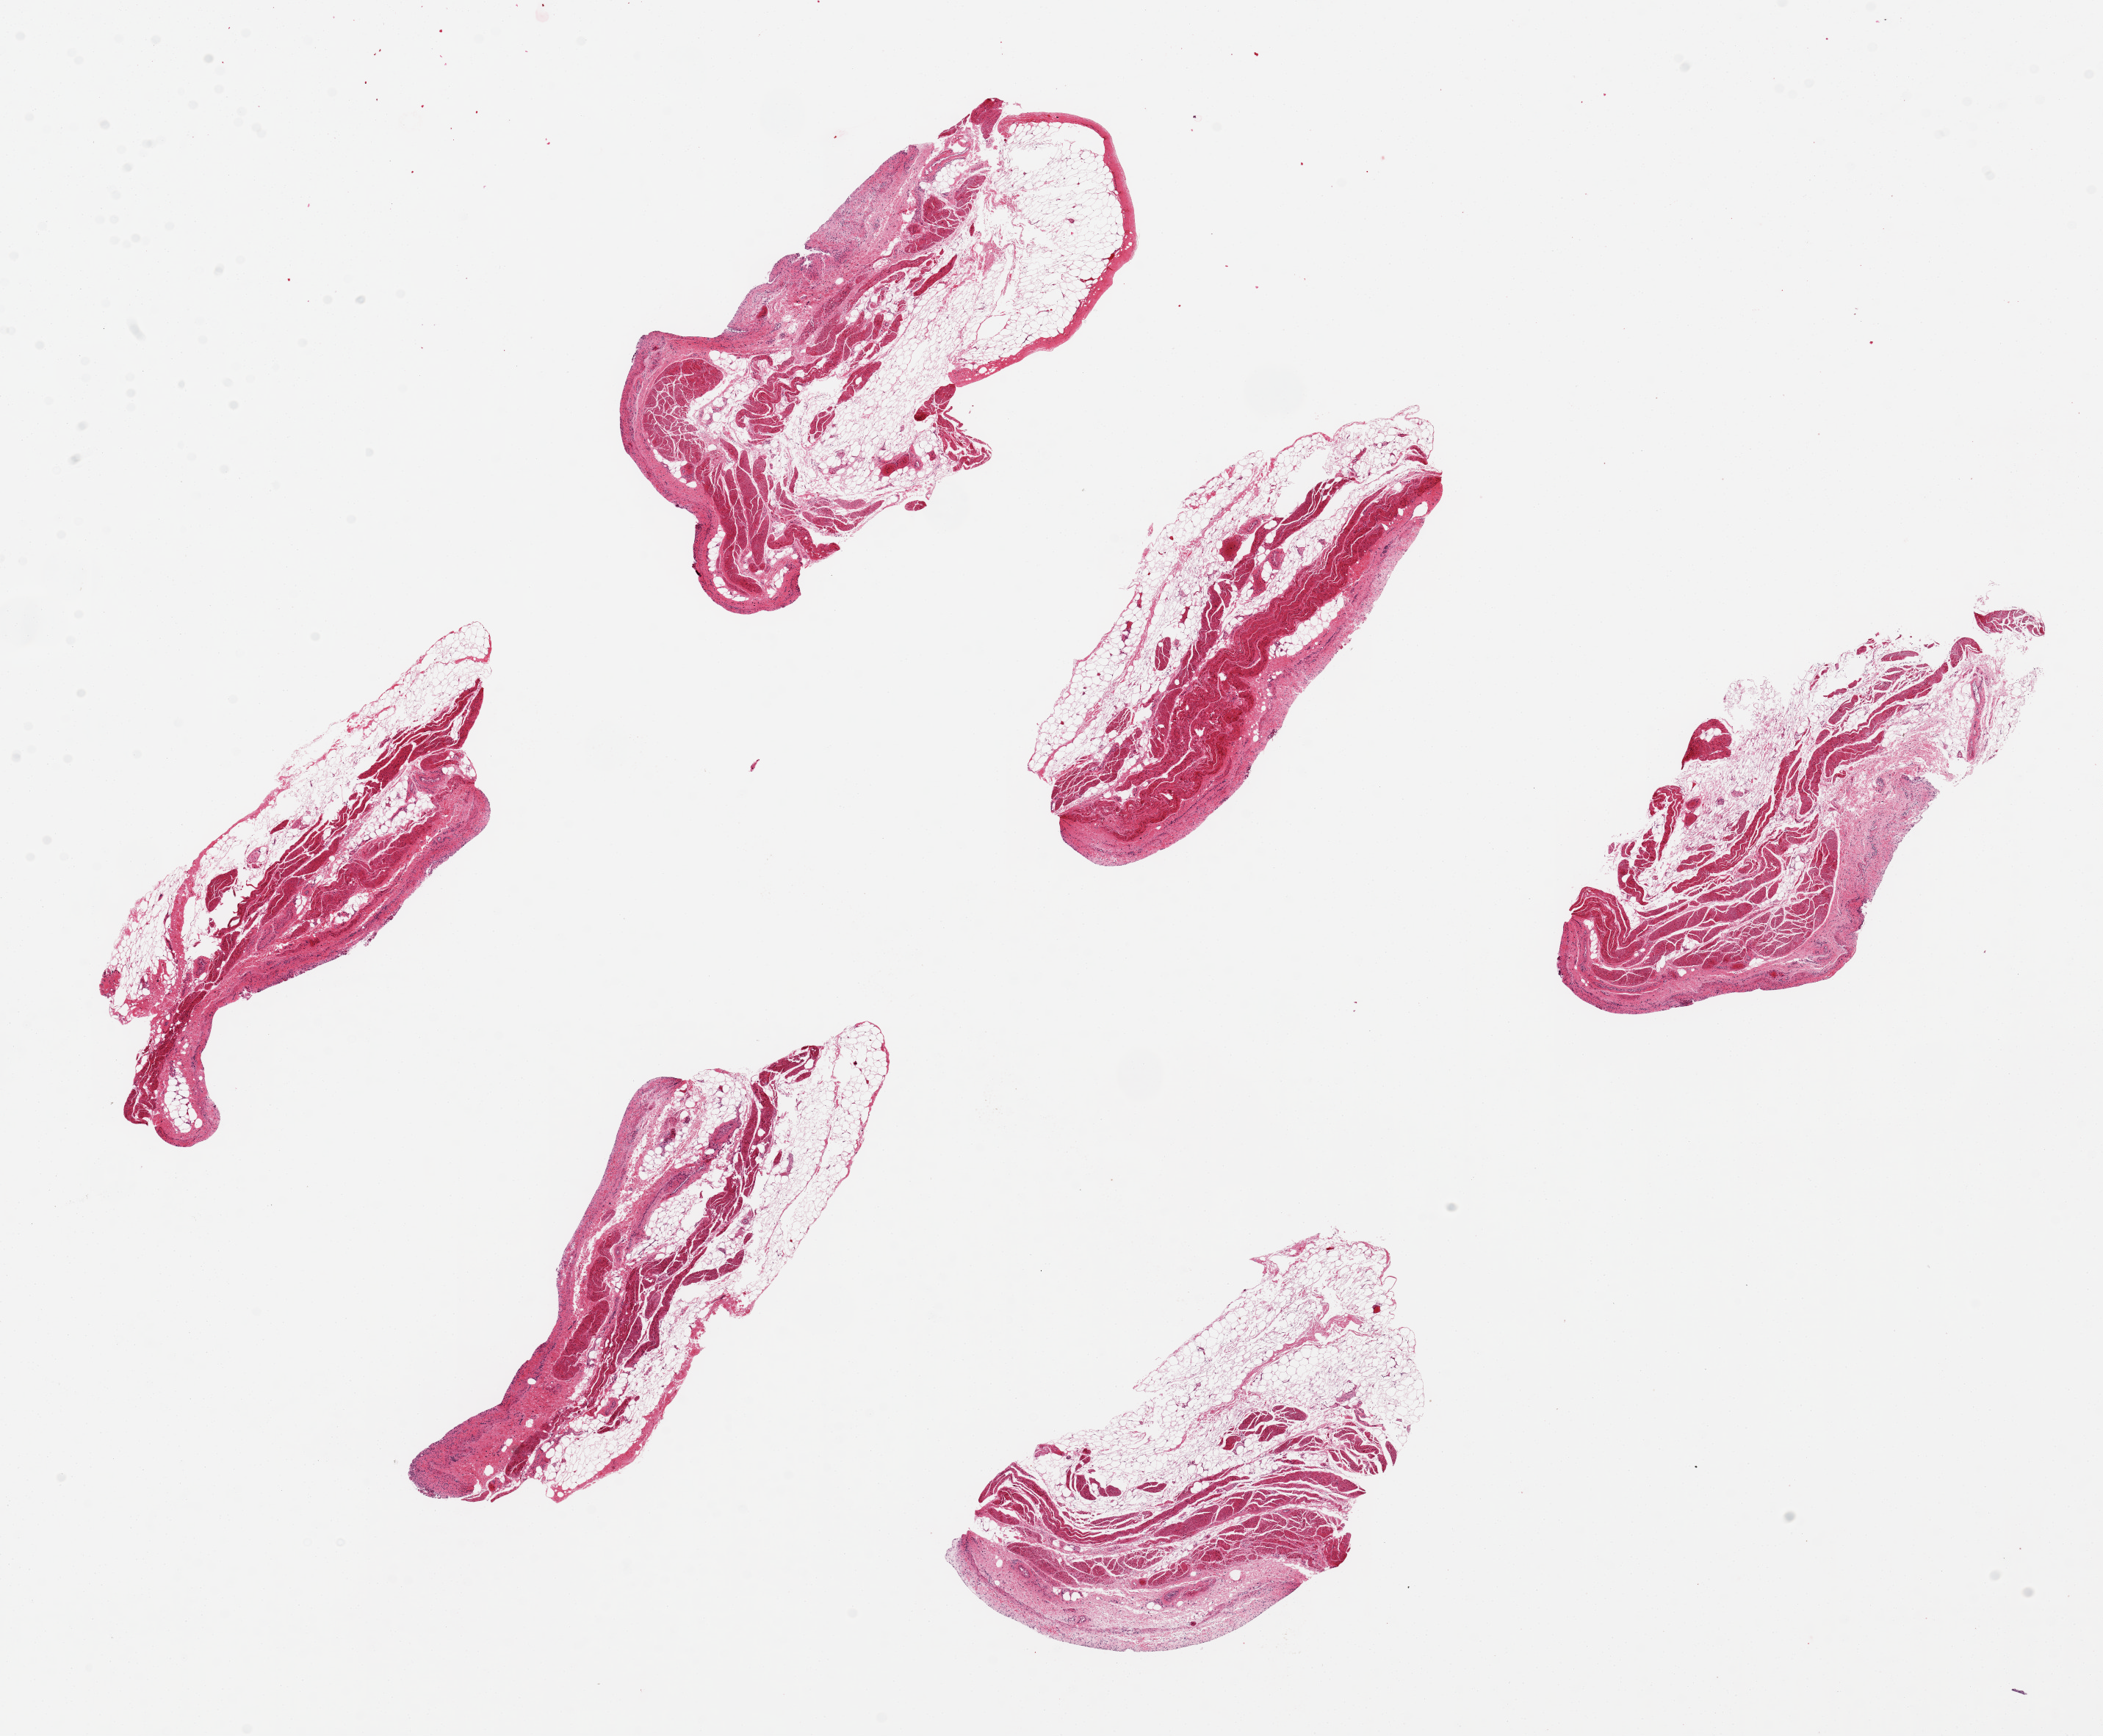
Digitized H&E-stained section — shown as a low-resolution overview of the whole scanned area (about 22.6 x 18.7 mm, slide scanned at 20x); PAXgene-fixed, paraffin-embedded tissue; target tissue: urinary bladder; tissue donor sample. Donor: female.
Review note (as recorded): 6 pieces, ~6x2.5mm, urothelium totally sloughed.